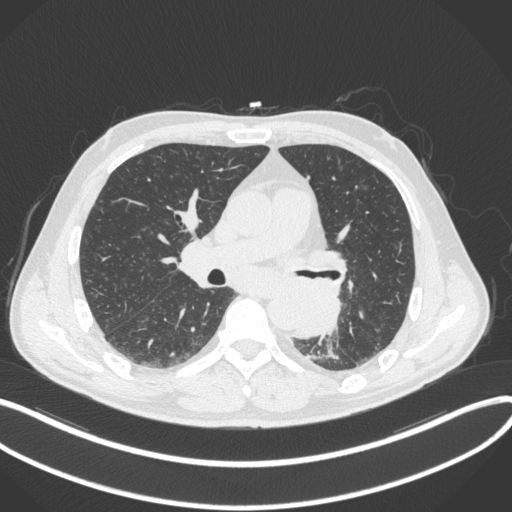
Chest CT, one axial slice. Position 188 of 328 along the scan axis. Reconstruction kernel B31f. Lung window (W 1500 / L -600 HU). 1 mm slice thickness. 512 × 512 image matrix, field of view 400 × 400 mm. Male patient, age 59 years. From the clinical record (not read from this slice): clinical TNM (as recorded): T2a N2 M0.
Structures marked on this image (bounding box drawn by a radiologist):
- lung tumour (recorded histology: squamous cell carcinoma): bounding box <288,280,346,342> (left, top, right, bottom; pixels)